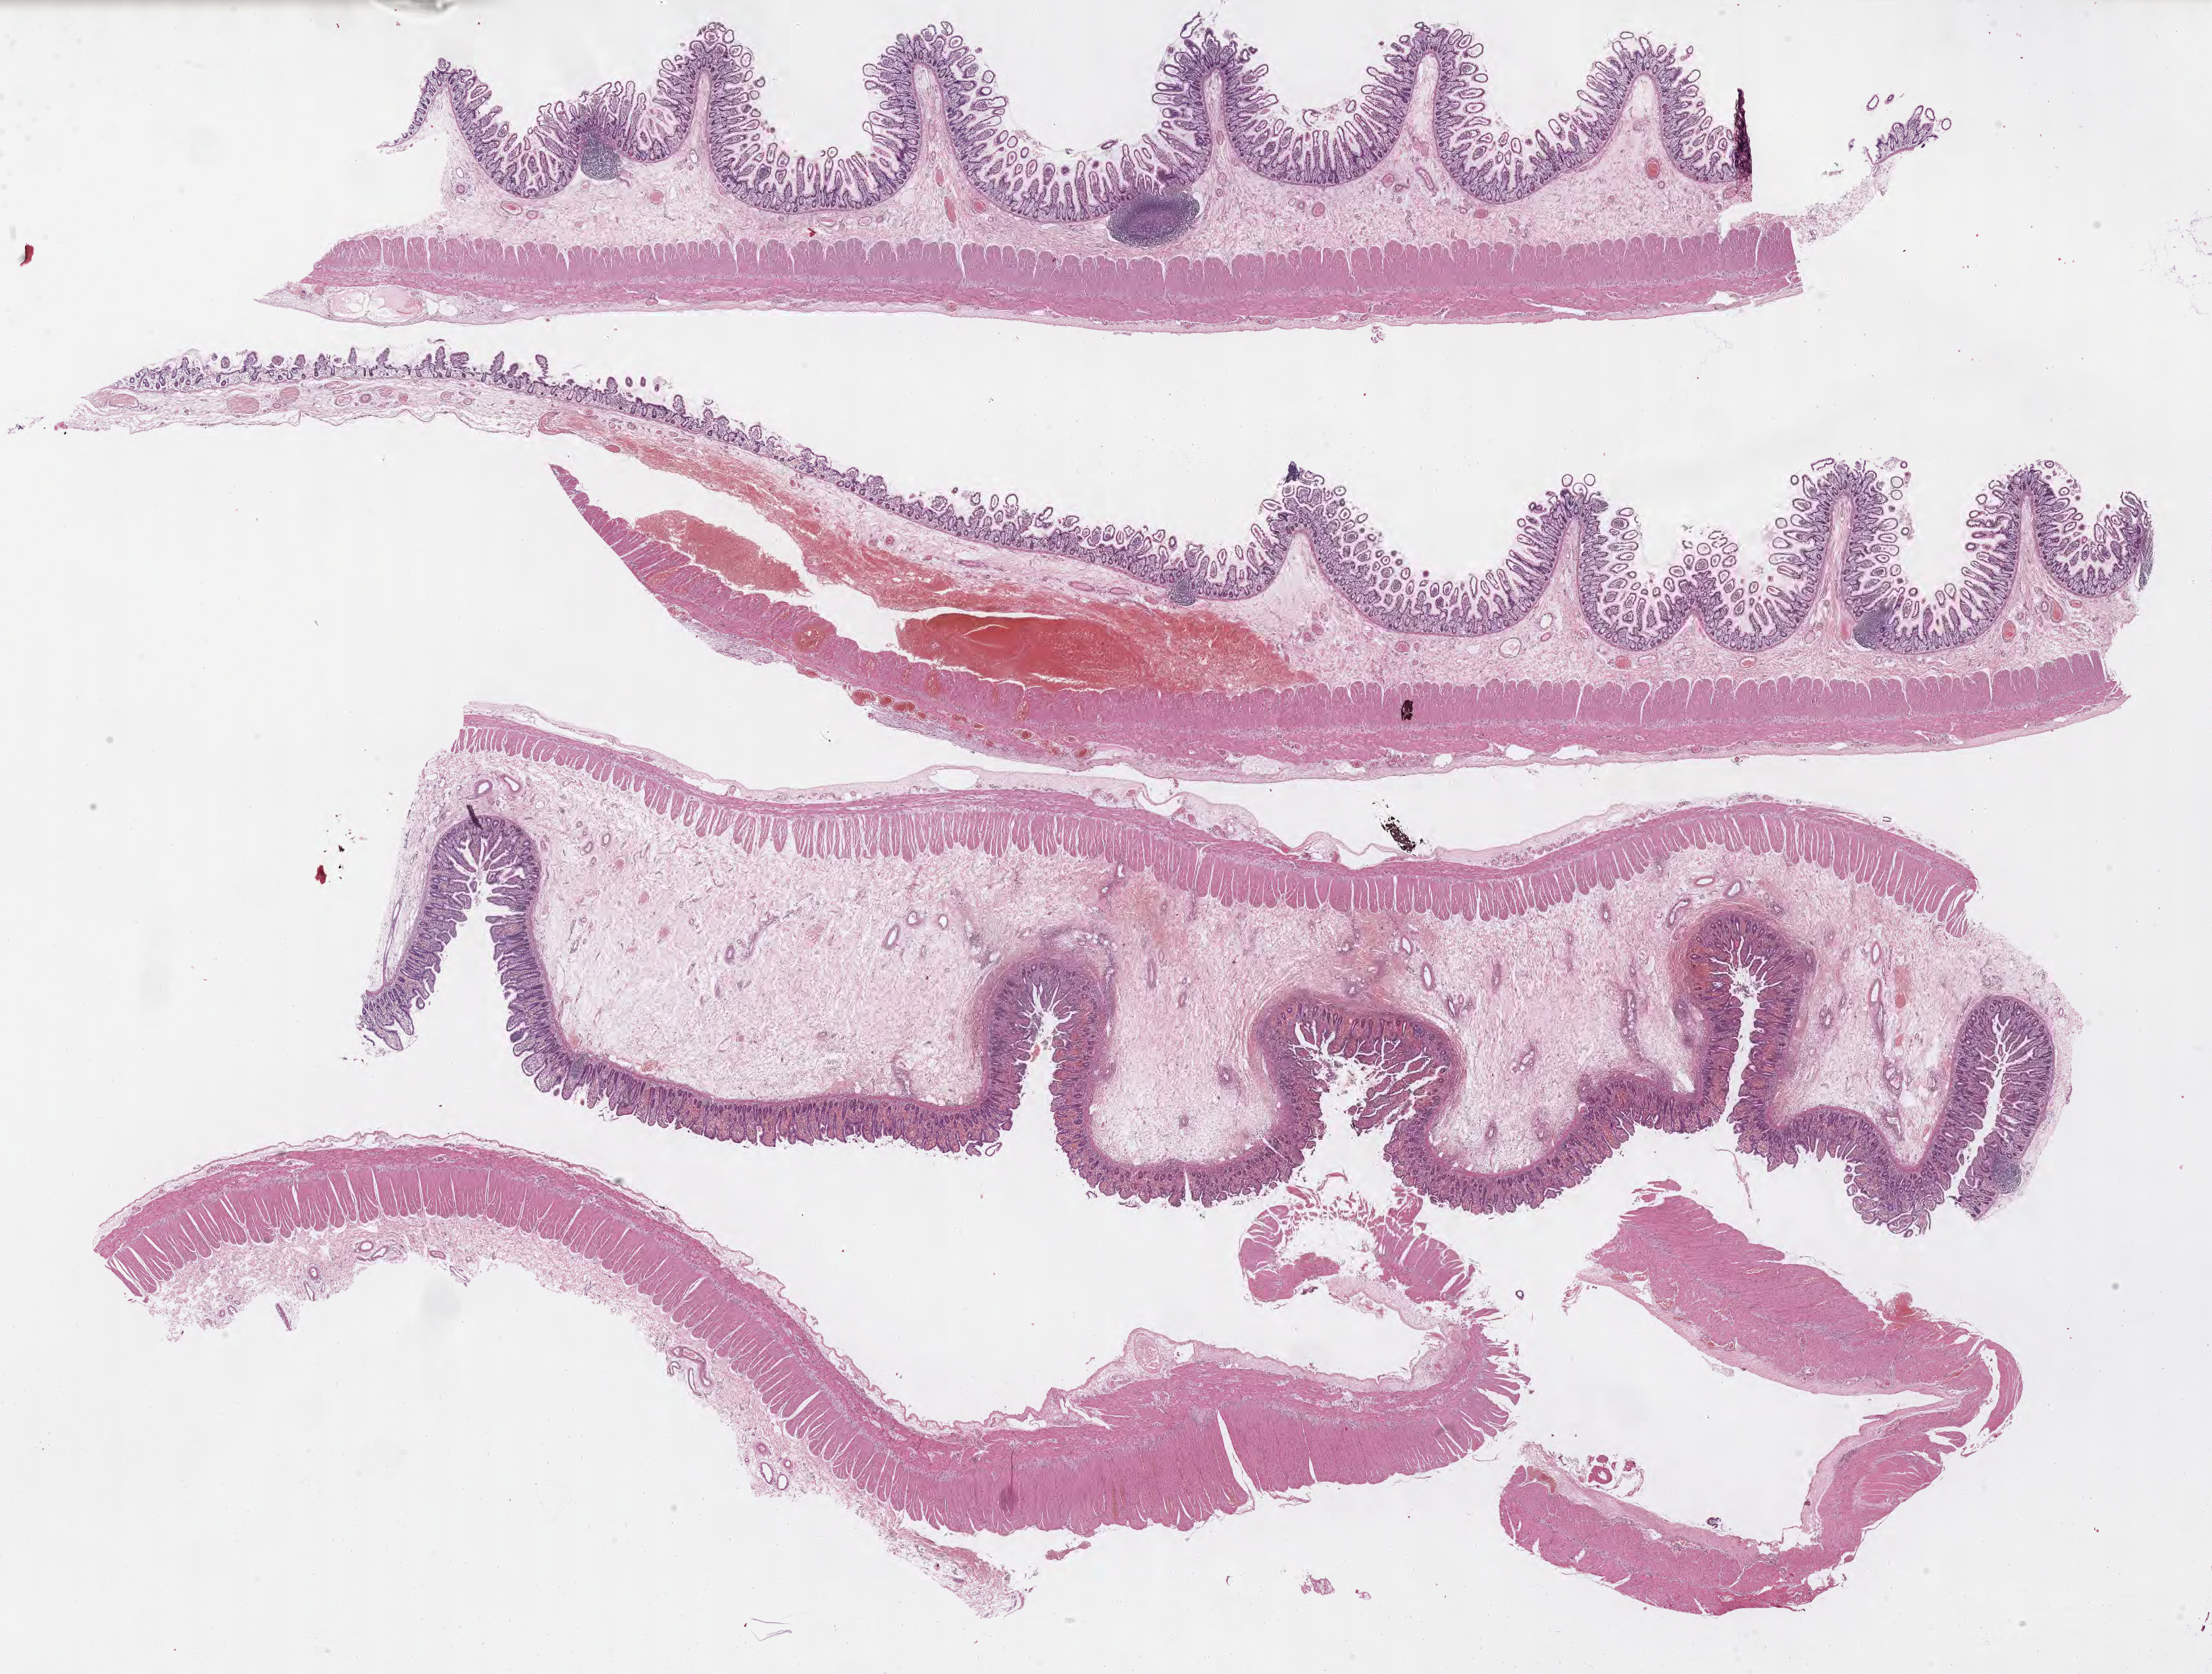
Digitized hematoxylin and eosin (H&E)-stained section — shown as a low-resolution overview of the whole scanned area (about 27.2 x 20.6 mm). Tumor tissue. Patient: female, aged 27.
• diagnosis: Burkitt lymphoma, NOS